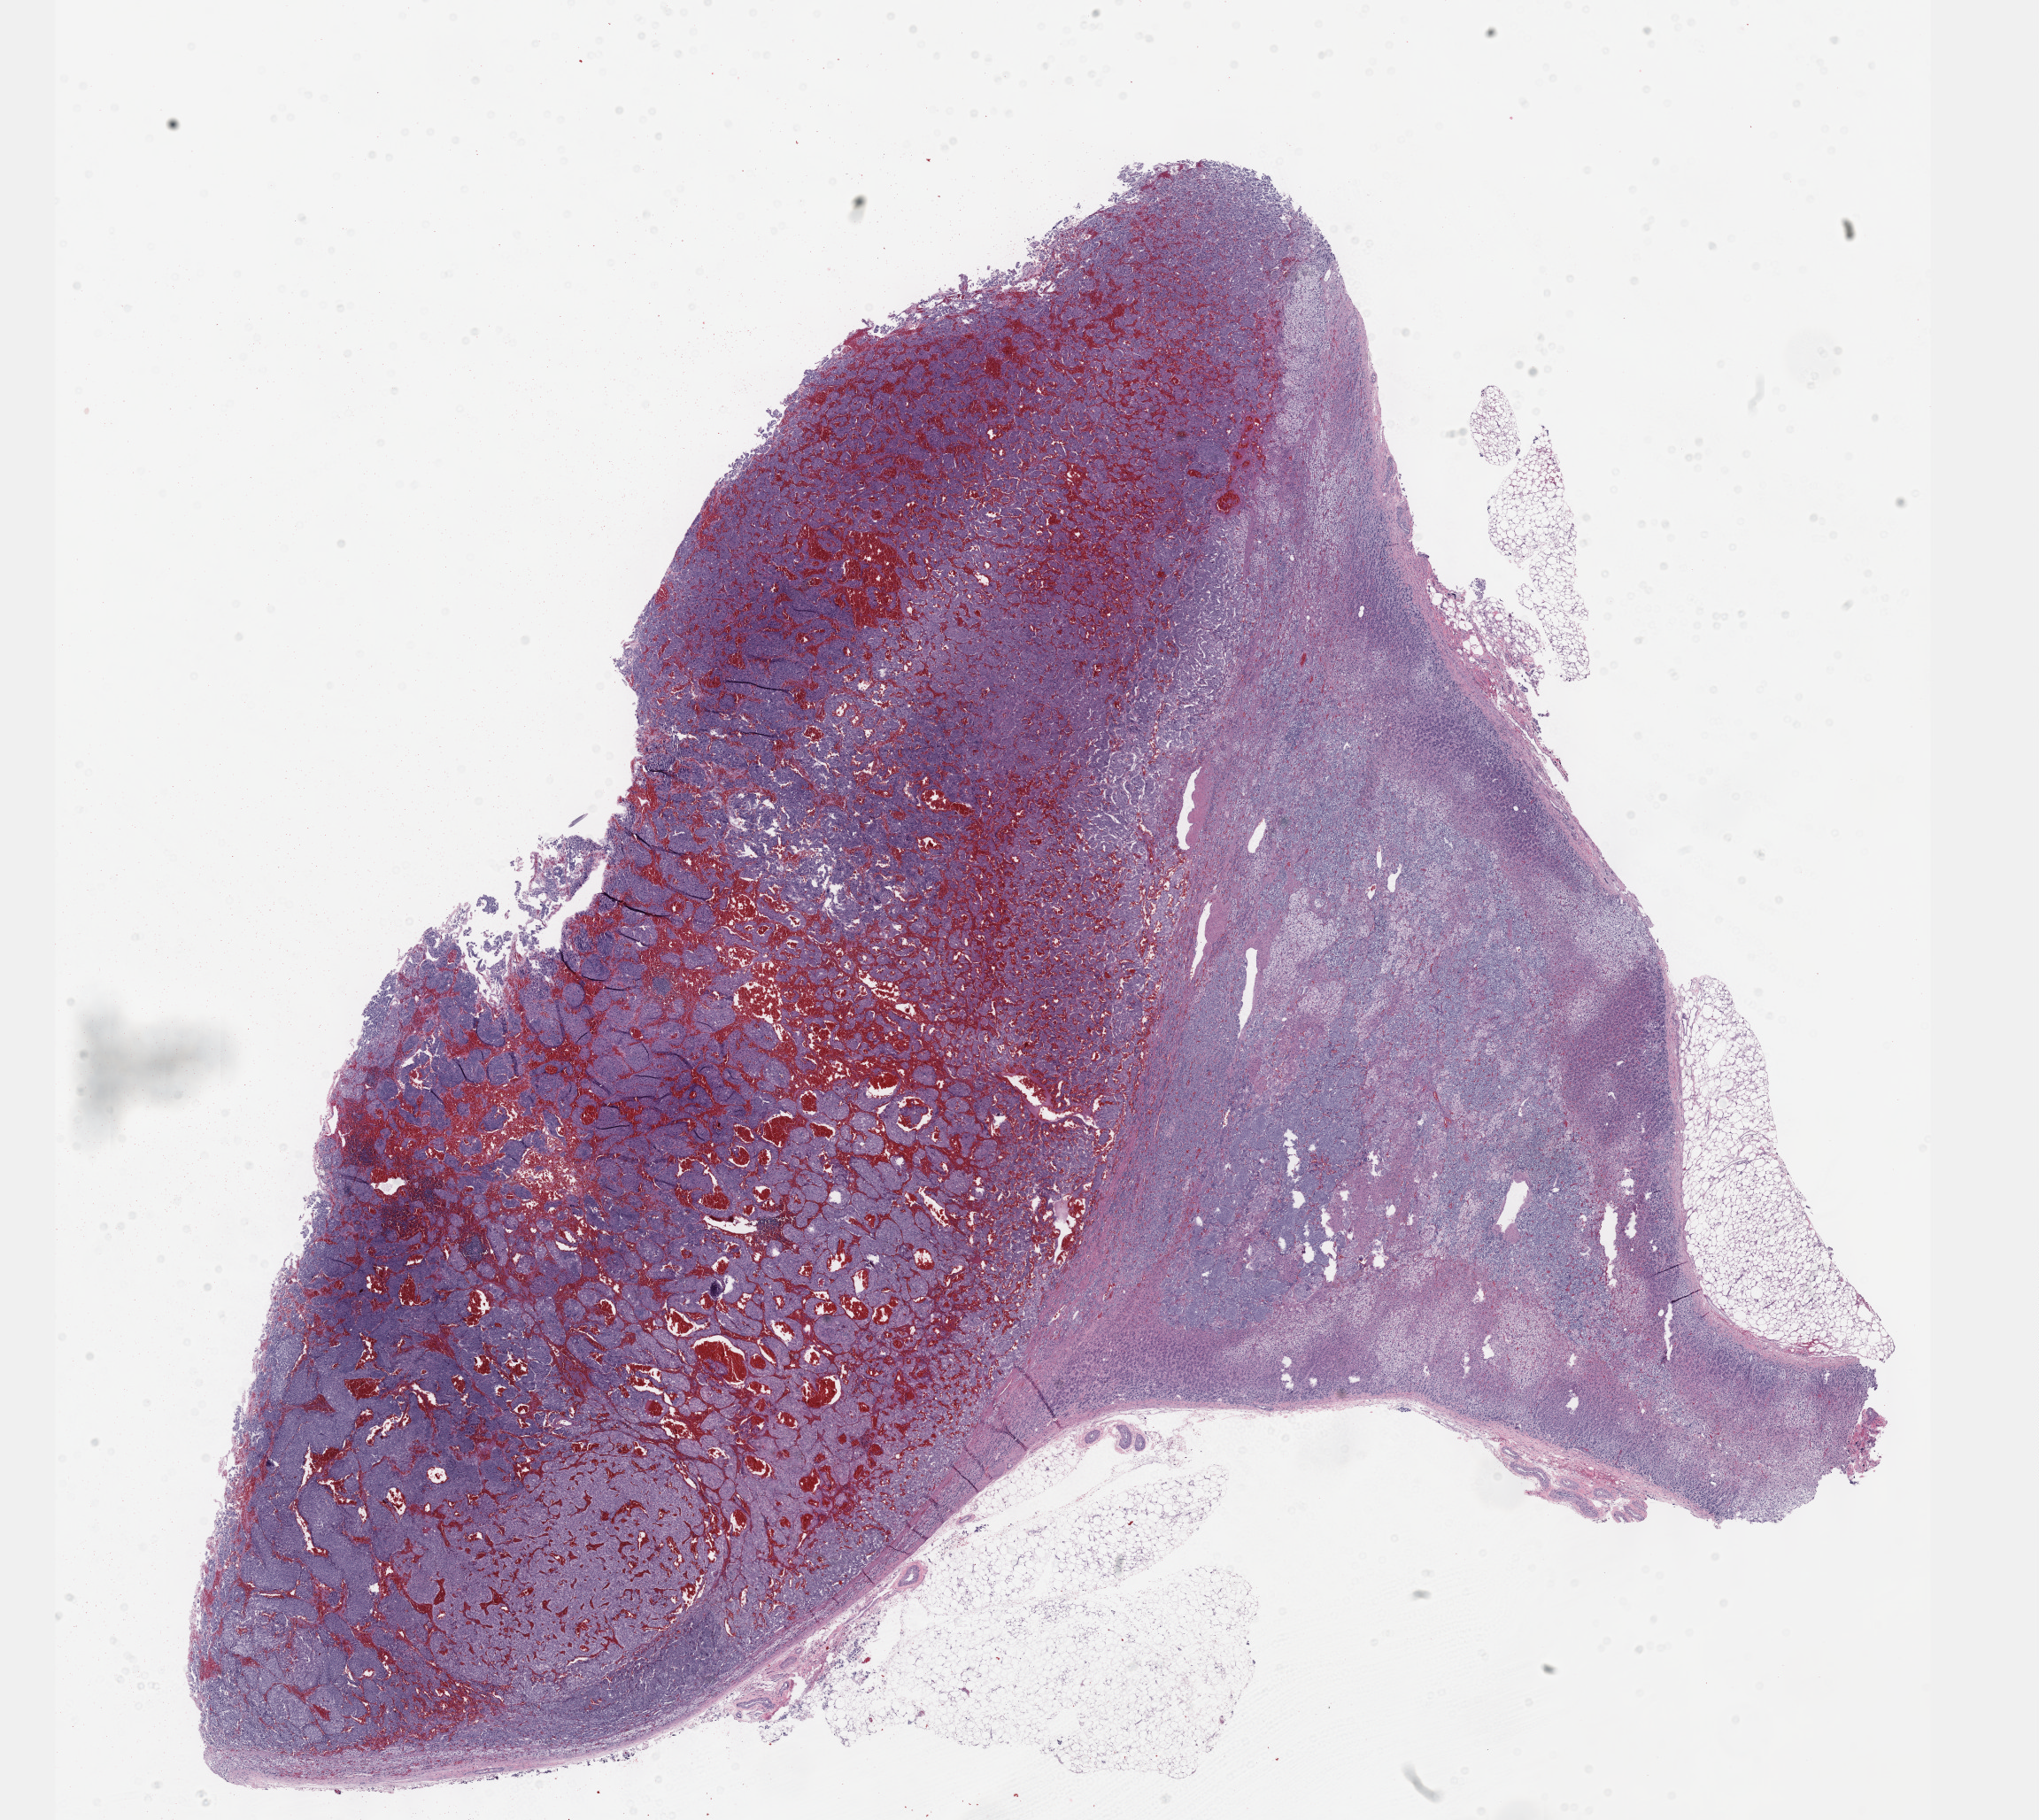
Whole-slide histology image, H&E — a low-resolution overview of the entire scanned area, about 18.6 x 16.6 mm (acquisition: 40x scan), FFPE section, sample: primary tumour, adrenal gland. Female patient; age at initial diagnosis 46 years.
Laterality: right. Histologic diagnosis: Pheochromocytoma, NOS.